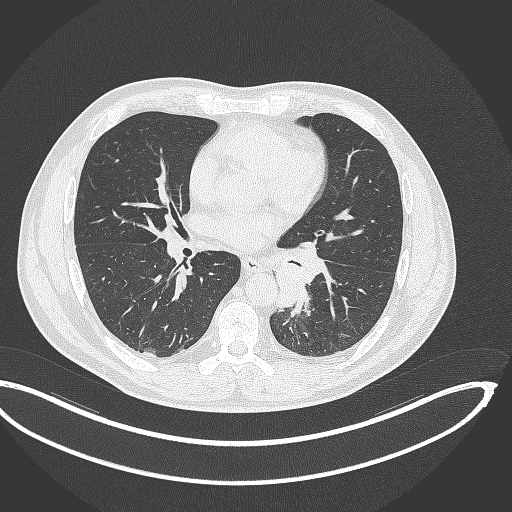
Chest CT, one axial slice; slice 174 of 362 in the series (ordered by position); reconstruction kernel B70f; 120 kVp; lung window (W 1500 / L -600 HU); 512 × 512 image matrix, field of view 442 × 442 mm. Male patient, age 50 years. Case-level facts recorded for this patient, not image findings: clinical TNM (as recorded): T2a N3 M0.
Structures marked on this image (rectangle marked by the reading radiologist):
- lung tumour (recorded histology: squamous cell carcinoma): box from (x=269, y=237) to (x=325, y=313) px